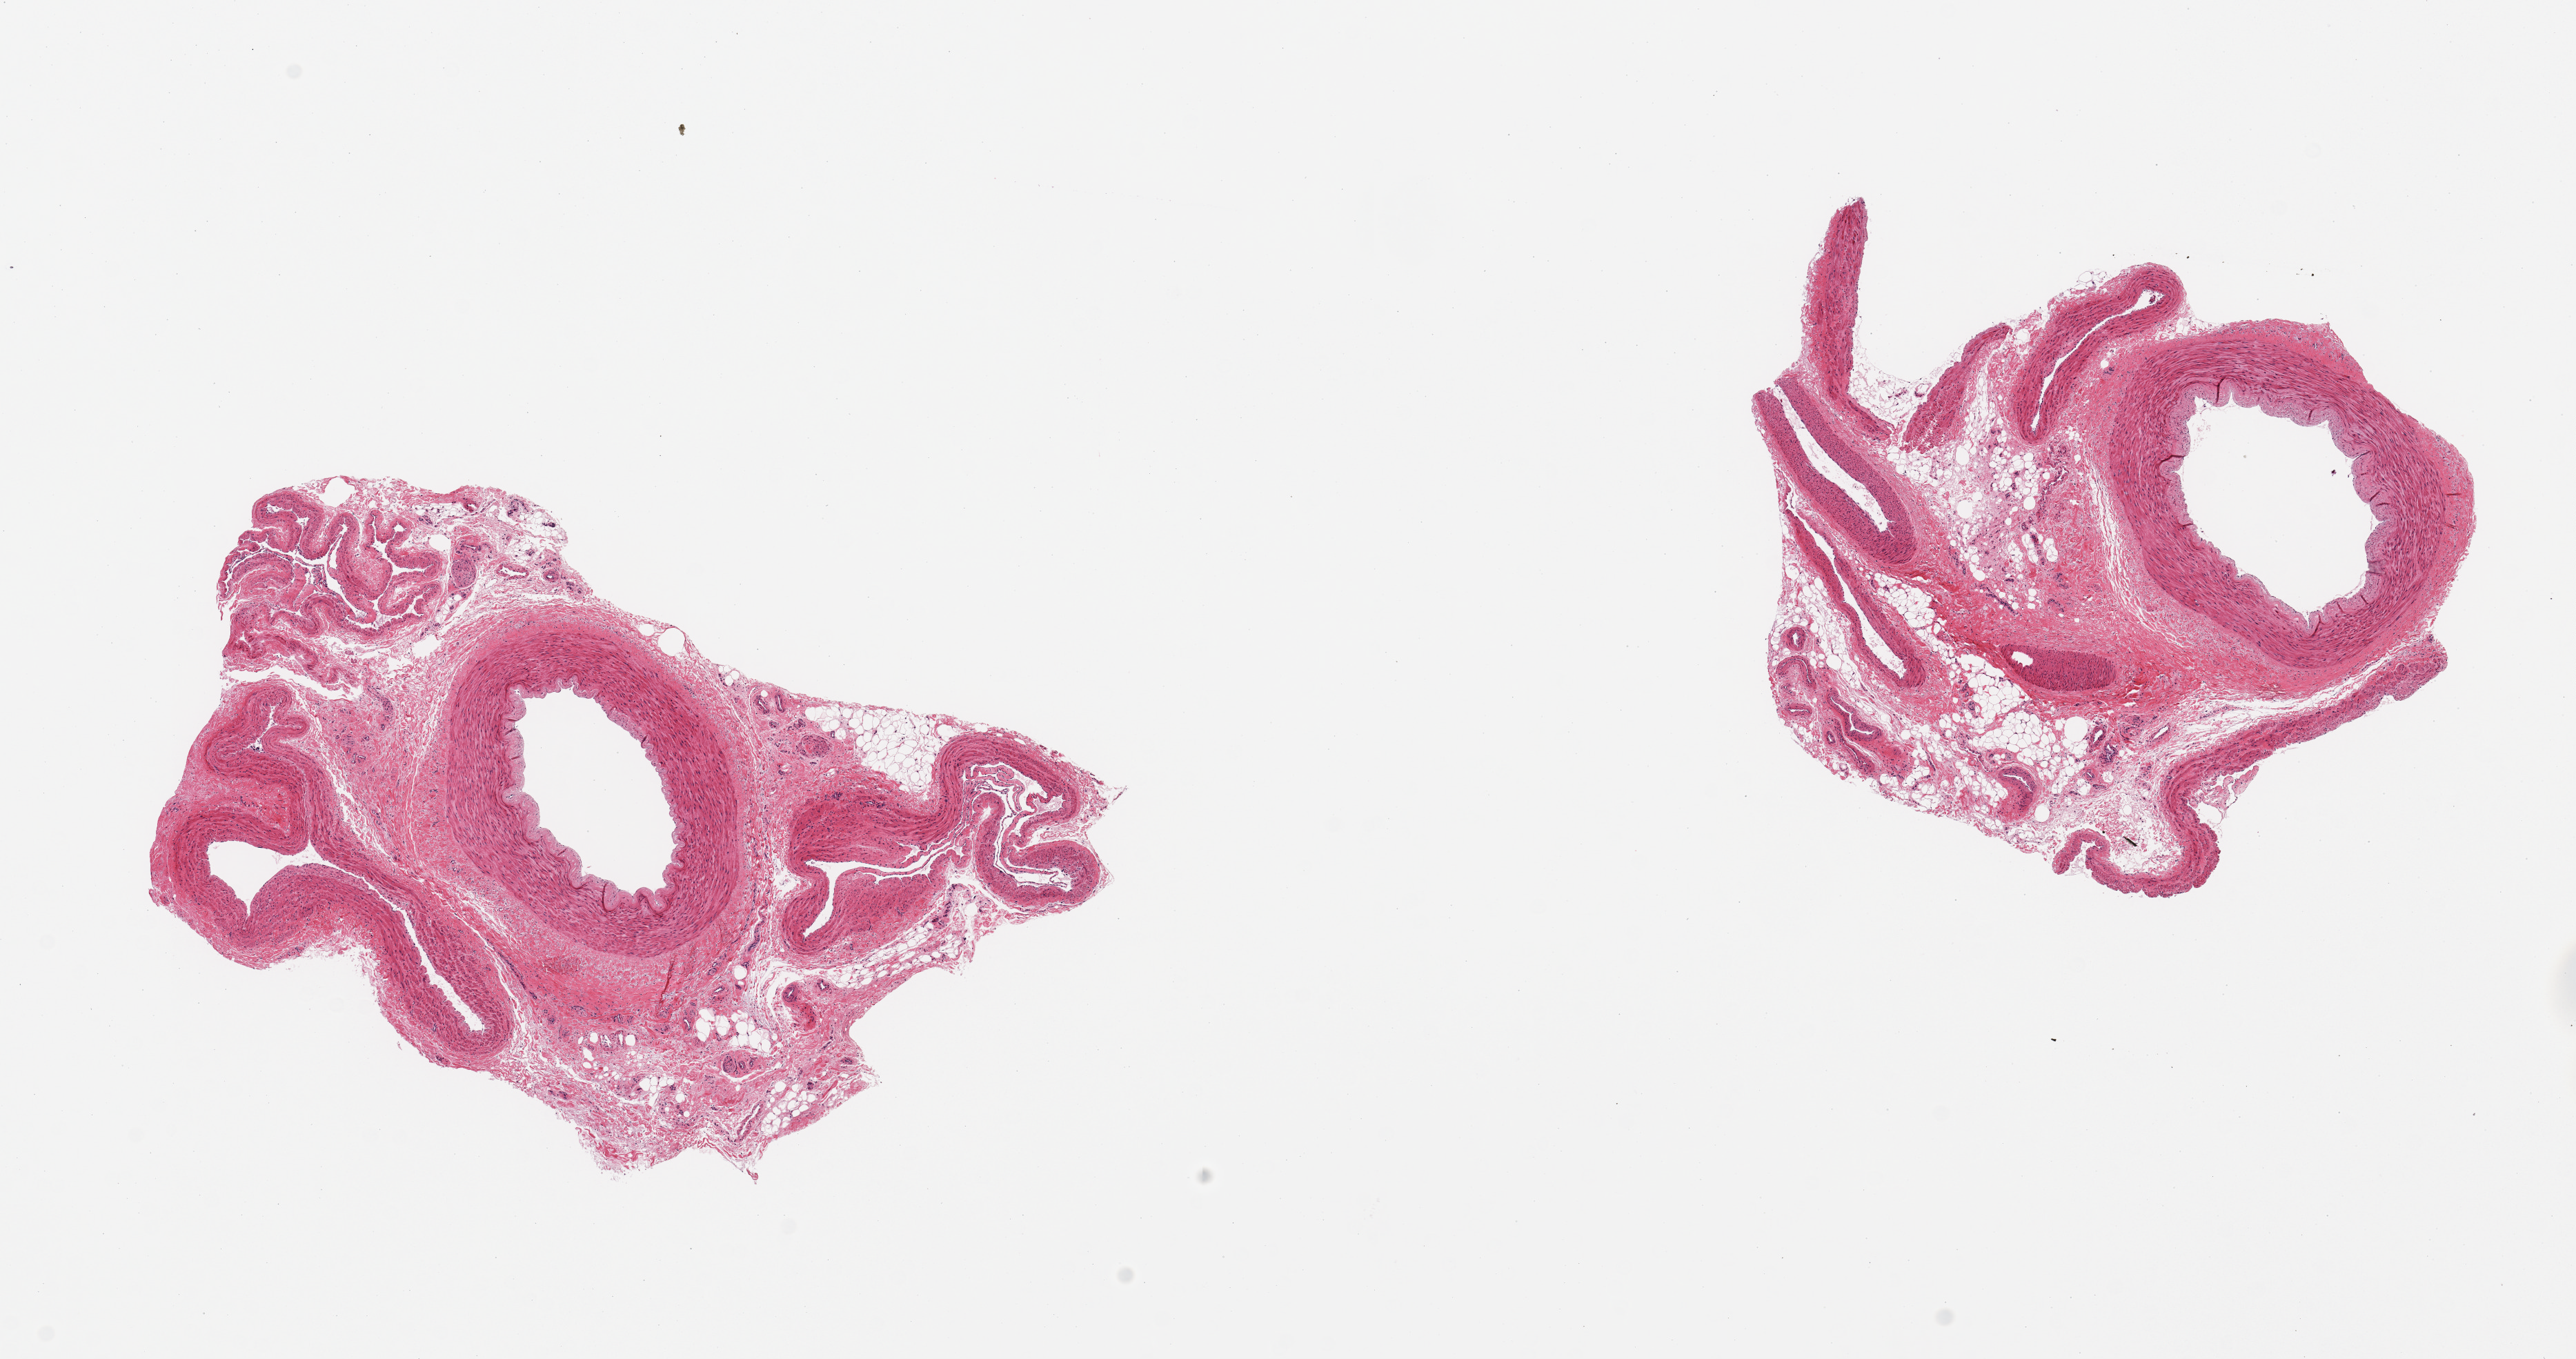
Whole-slide image, hematoxylin and eosin (H&E) stain — low-resolution overview of the scanned area, about 14.8 x 7.8 mm; PAXgene-fixed paraffin-embedded (PFPE) section; target tissue: tibial artery; donor tissue sample. Donor: male.
Pathologist's review note for this sample: 2 pieces, ~50% adherent venous/adipose nubbins up to ~2mm.